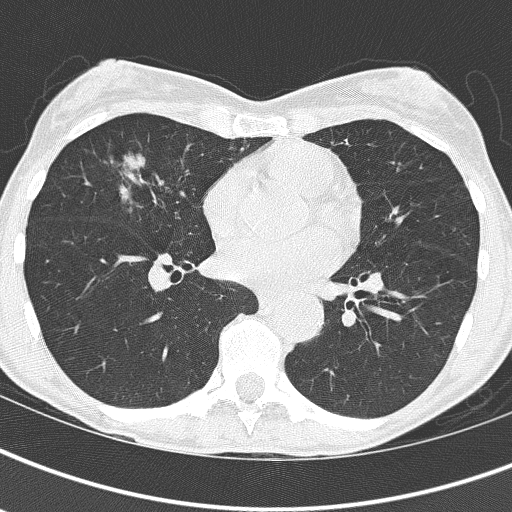
Chest CT (low-dose screening protocol), one axial image, baseline annual screen, lung window (W 1500 / L -600 HU), 2 mm slice thickness, lung (sharp) reconstruction kernel (B60f), slice 91 of 161 in the series. Female participant, aged 67 years at enrolment. Current smoker at enrolment.
Expert-annotated lung lesion, bounding box (x1, y1, x2, y2) in pixels: (90, 137, 175, 217). Screening reader's record for this exam: no non-calcified nodule ≥4 mm recorded. Later outcome: lung cancer diagnosed 832 days after this screen — bronchiolo-alveolar adenocarcinoma, NOS, right middle lobe, well differentiated (G1), stage IA (AJCC 6th edition), 25 mm at pathology.